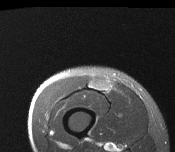
MRI of an extremity soft-tissue mass, one axial slice; position 32 of 116 along the scan axis; T2-weighted fat-saturated; MR volume resampled by the dataset authors to the PET/CT grid (not the native acquisition matrix); 3.27 mm slice thickness; 175 × 152 image matrix, field of view 171 × 148 mm. Male patient. From the clinical record (not read from this slice): histological type: pleiomorphic leiomyosarcoma; grade: intermediate; site of the primary tumour: right thigh.
Annotated regions visible in this slice (expert contour drawn on MRI and transferred to this co-registered scan by the dataset authors):
- gross tumour volume including surrounding oedema: box from (x=88, y=79) to (x=110, y=93) px